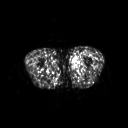
FDG PET of an extremity soft-tissue mass (from a PET/CT study), one axial slice; slice 233 of 311 in the series (ordered by position); 128 × 128 image matrix, field of view 500 × 500 mm. Patient: male, 29 years. Case-level facts recorded for this patient, not image findings: histological type: mixoid liposarcoma; grade: low; site of the primary tumour: left thigh.
Annotated regions visible in this slice (expert contour drawn on MRI and transferred to this co-registered scan by the dataset authors):
- gross tumour volume (mass): box from (x=71, y=56) to (x=82, y=69) px